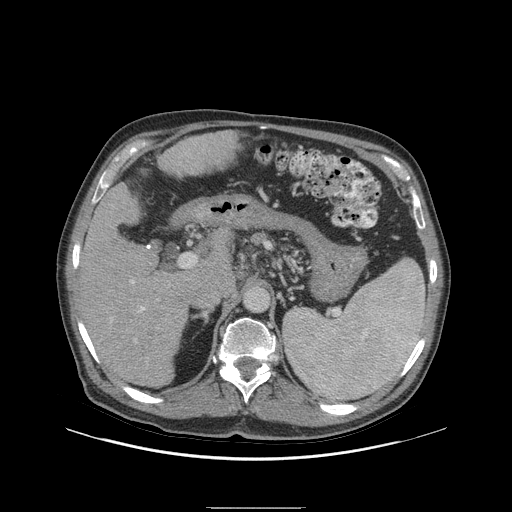
Contrast-enhanced abdominal CT (liver protocol), one axial slice. Position 55 of 105 along the scan axis. Reconstruction kernel STANDARD. Soft-tissue window (W 400 / L 40 HU). 2.5 mm slice thickness. 512 × 512 image matrix, field of view 440 × 440 mm. Case-level facts recorded for this patient, not image findings: diagnosis: hepatocellular carcinoma (patient treated with transarterial chemoembolisation; whether this scan precedes or follows treatment is not stated here); TNM stage (as recorded): Stage-I; Child-Pugh class: A; tumour size: 5.1 cm.
Outlined on this slice (semi-automatically segmented with operator editing):
- liver parenchyma outside the tumour (the mass and vessels are separate outlines, so this box may not span the whole liver): box from (x=74, y=184) to (x=196, y=386) px
- liver vessels: (x=92, y=245)–(x=150, y=362)